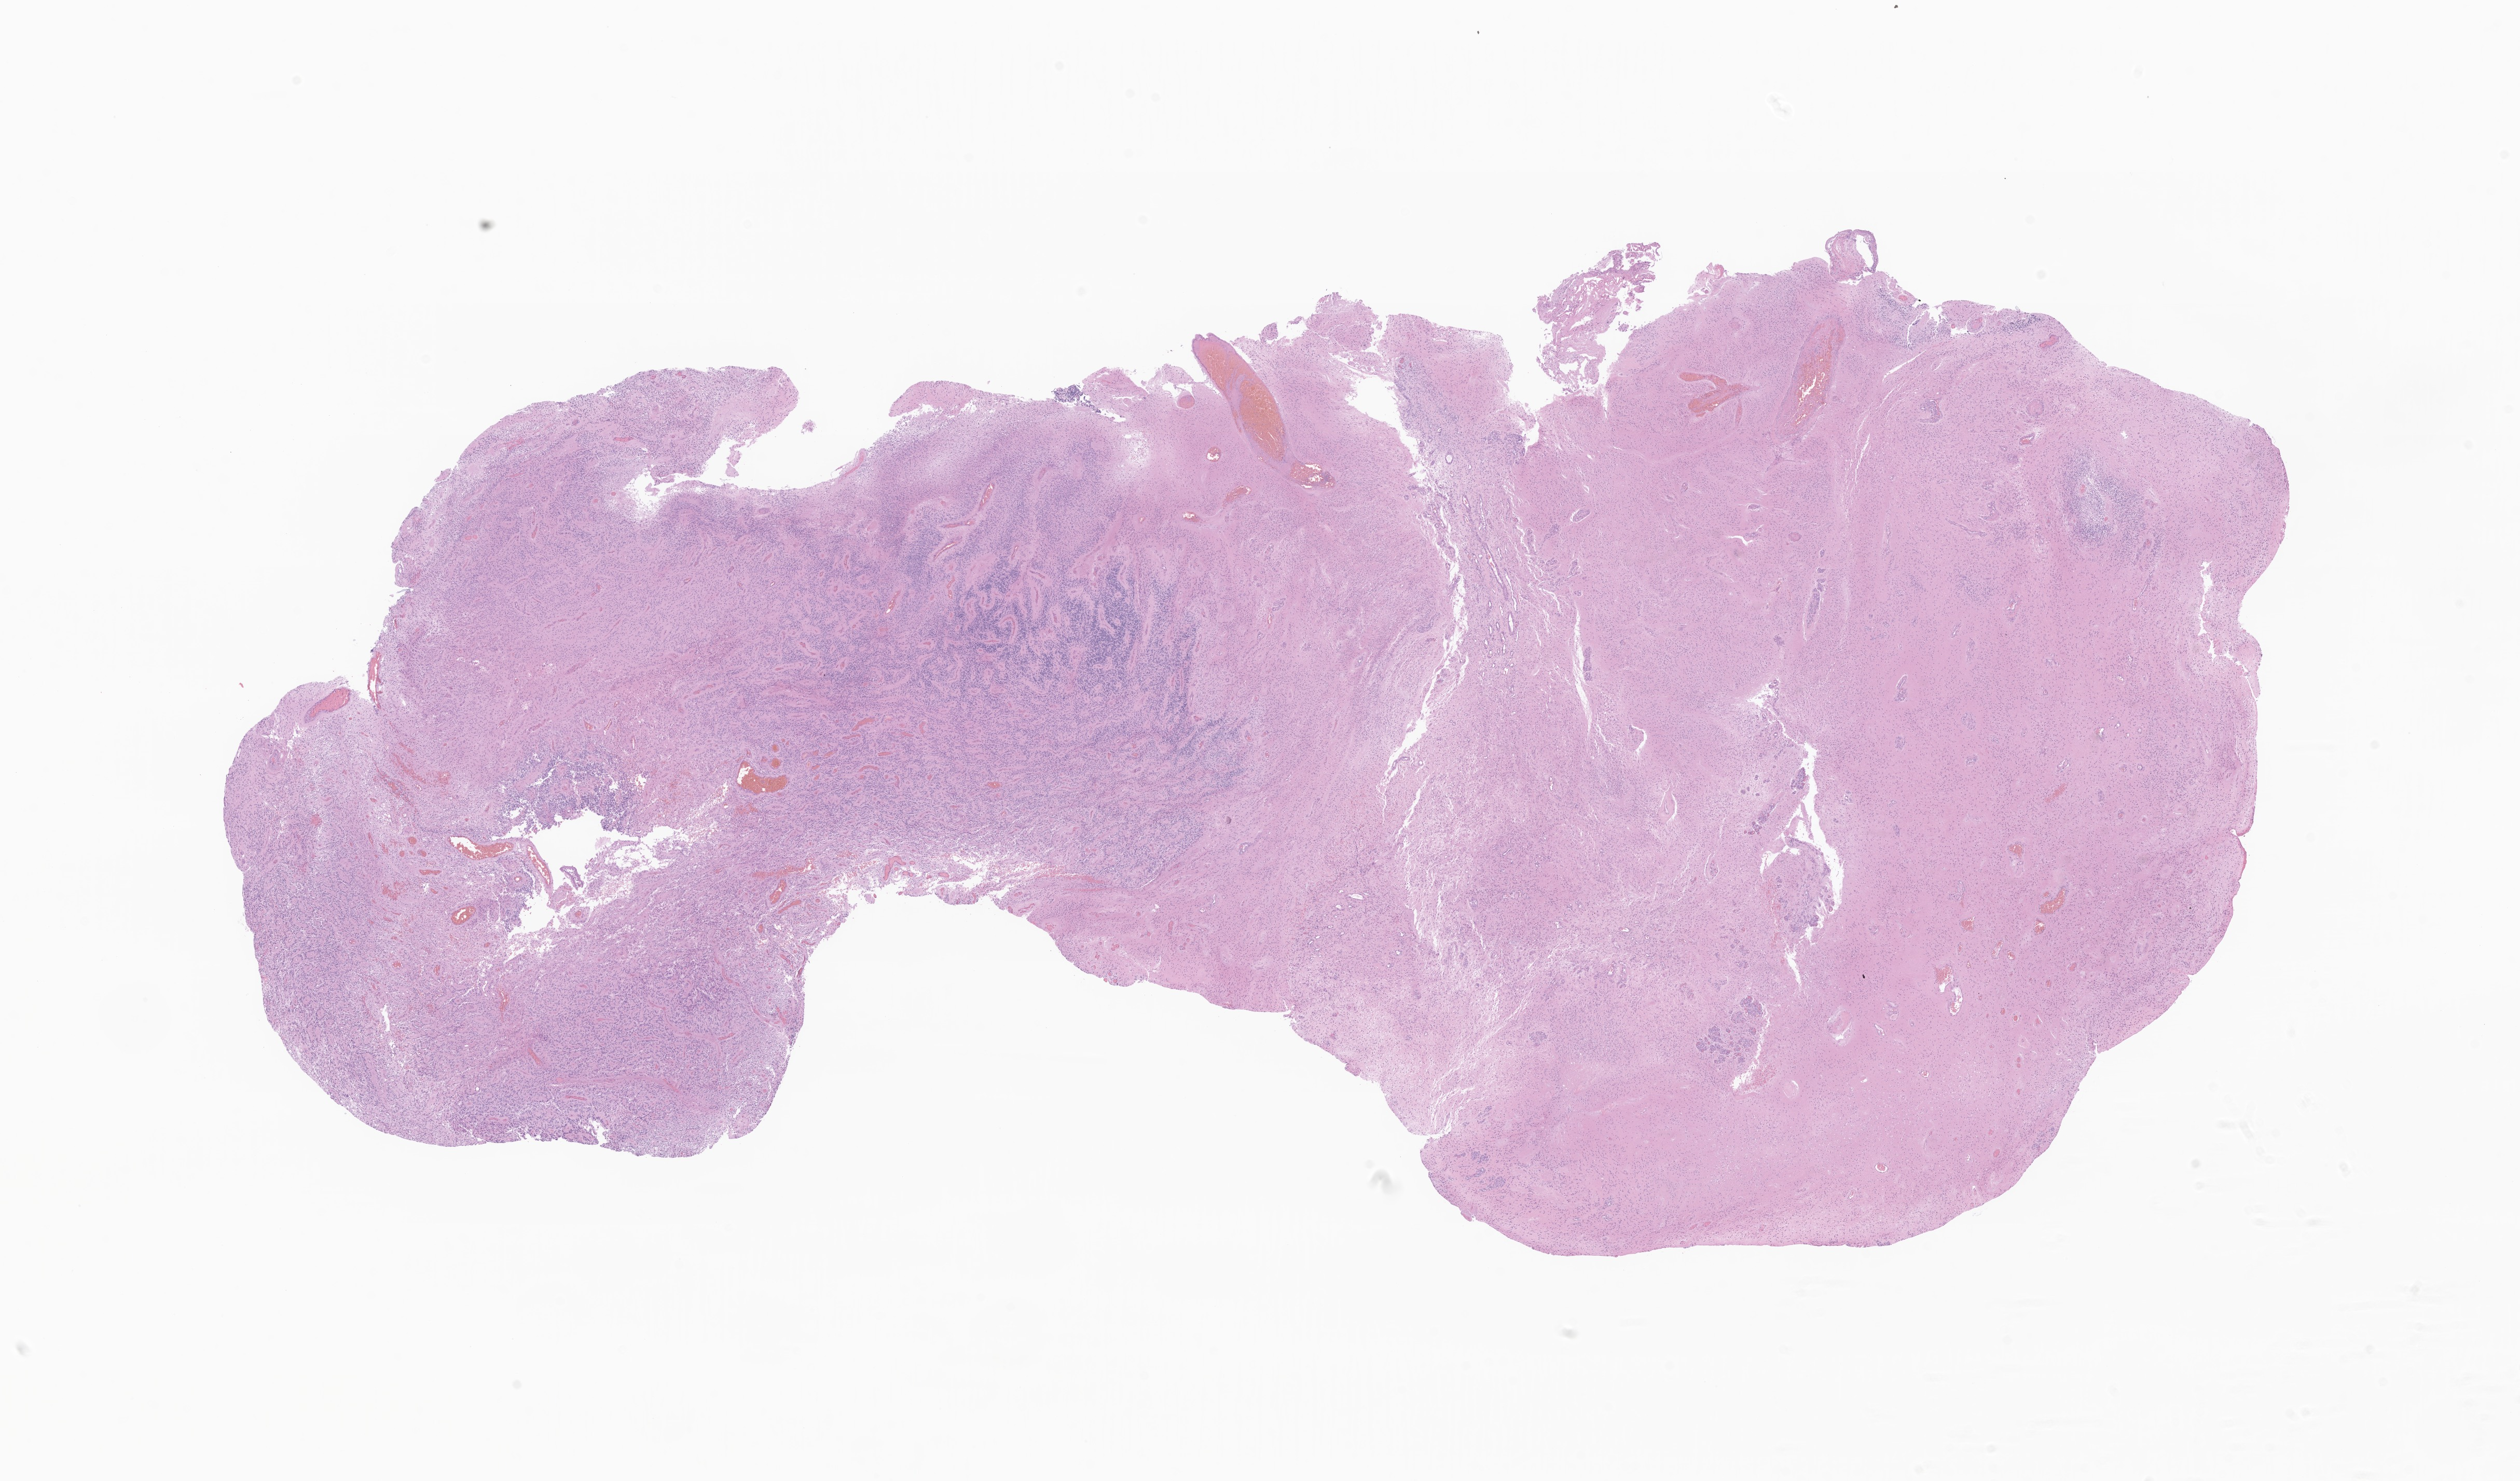
Whole-slide image, H&E stain of tumor tissue from the brain — shown as a low-resolution overview of the whole scanned area (about 20.5 x 12.0 mm). Formalin-fixed paraffin-embedded section. Patient male; age 72 months (6 years).
Recorded diagnosis: Ependymoma, NOS.